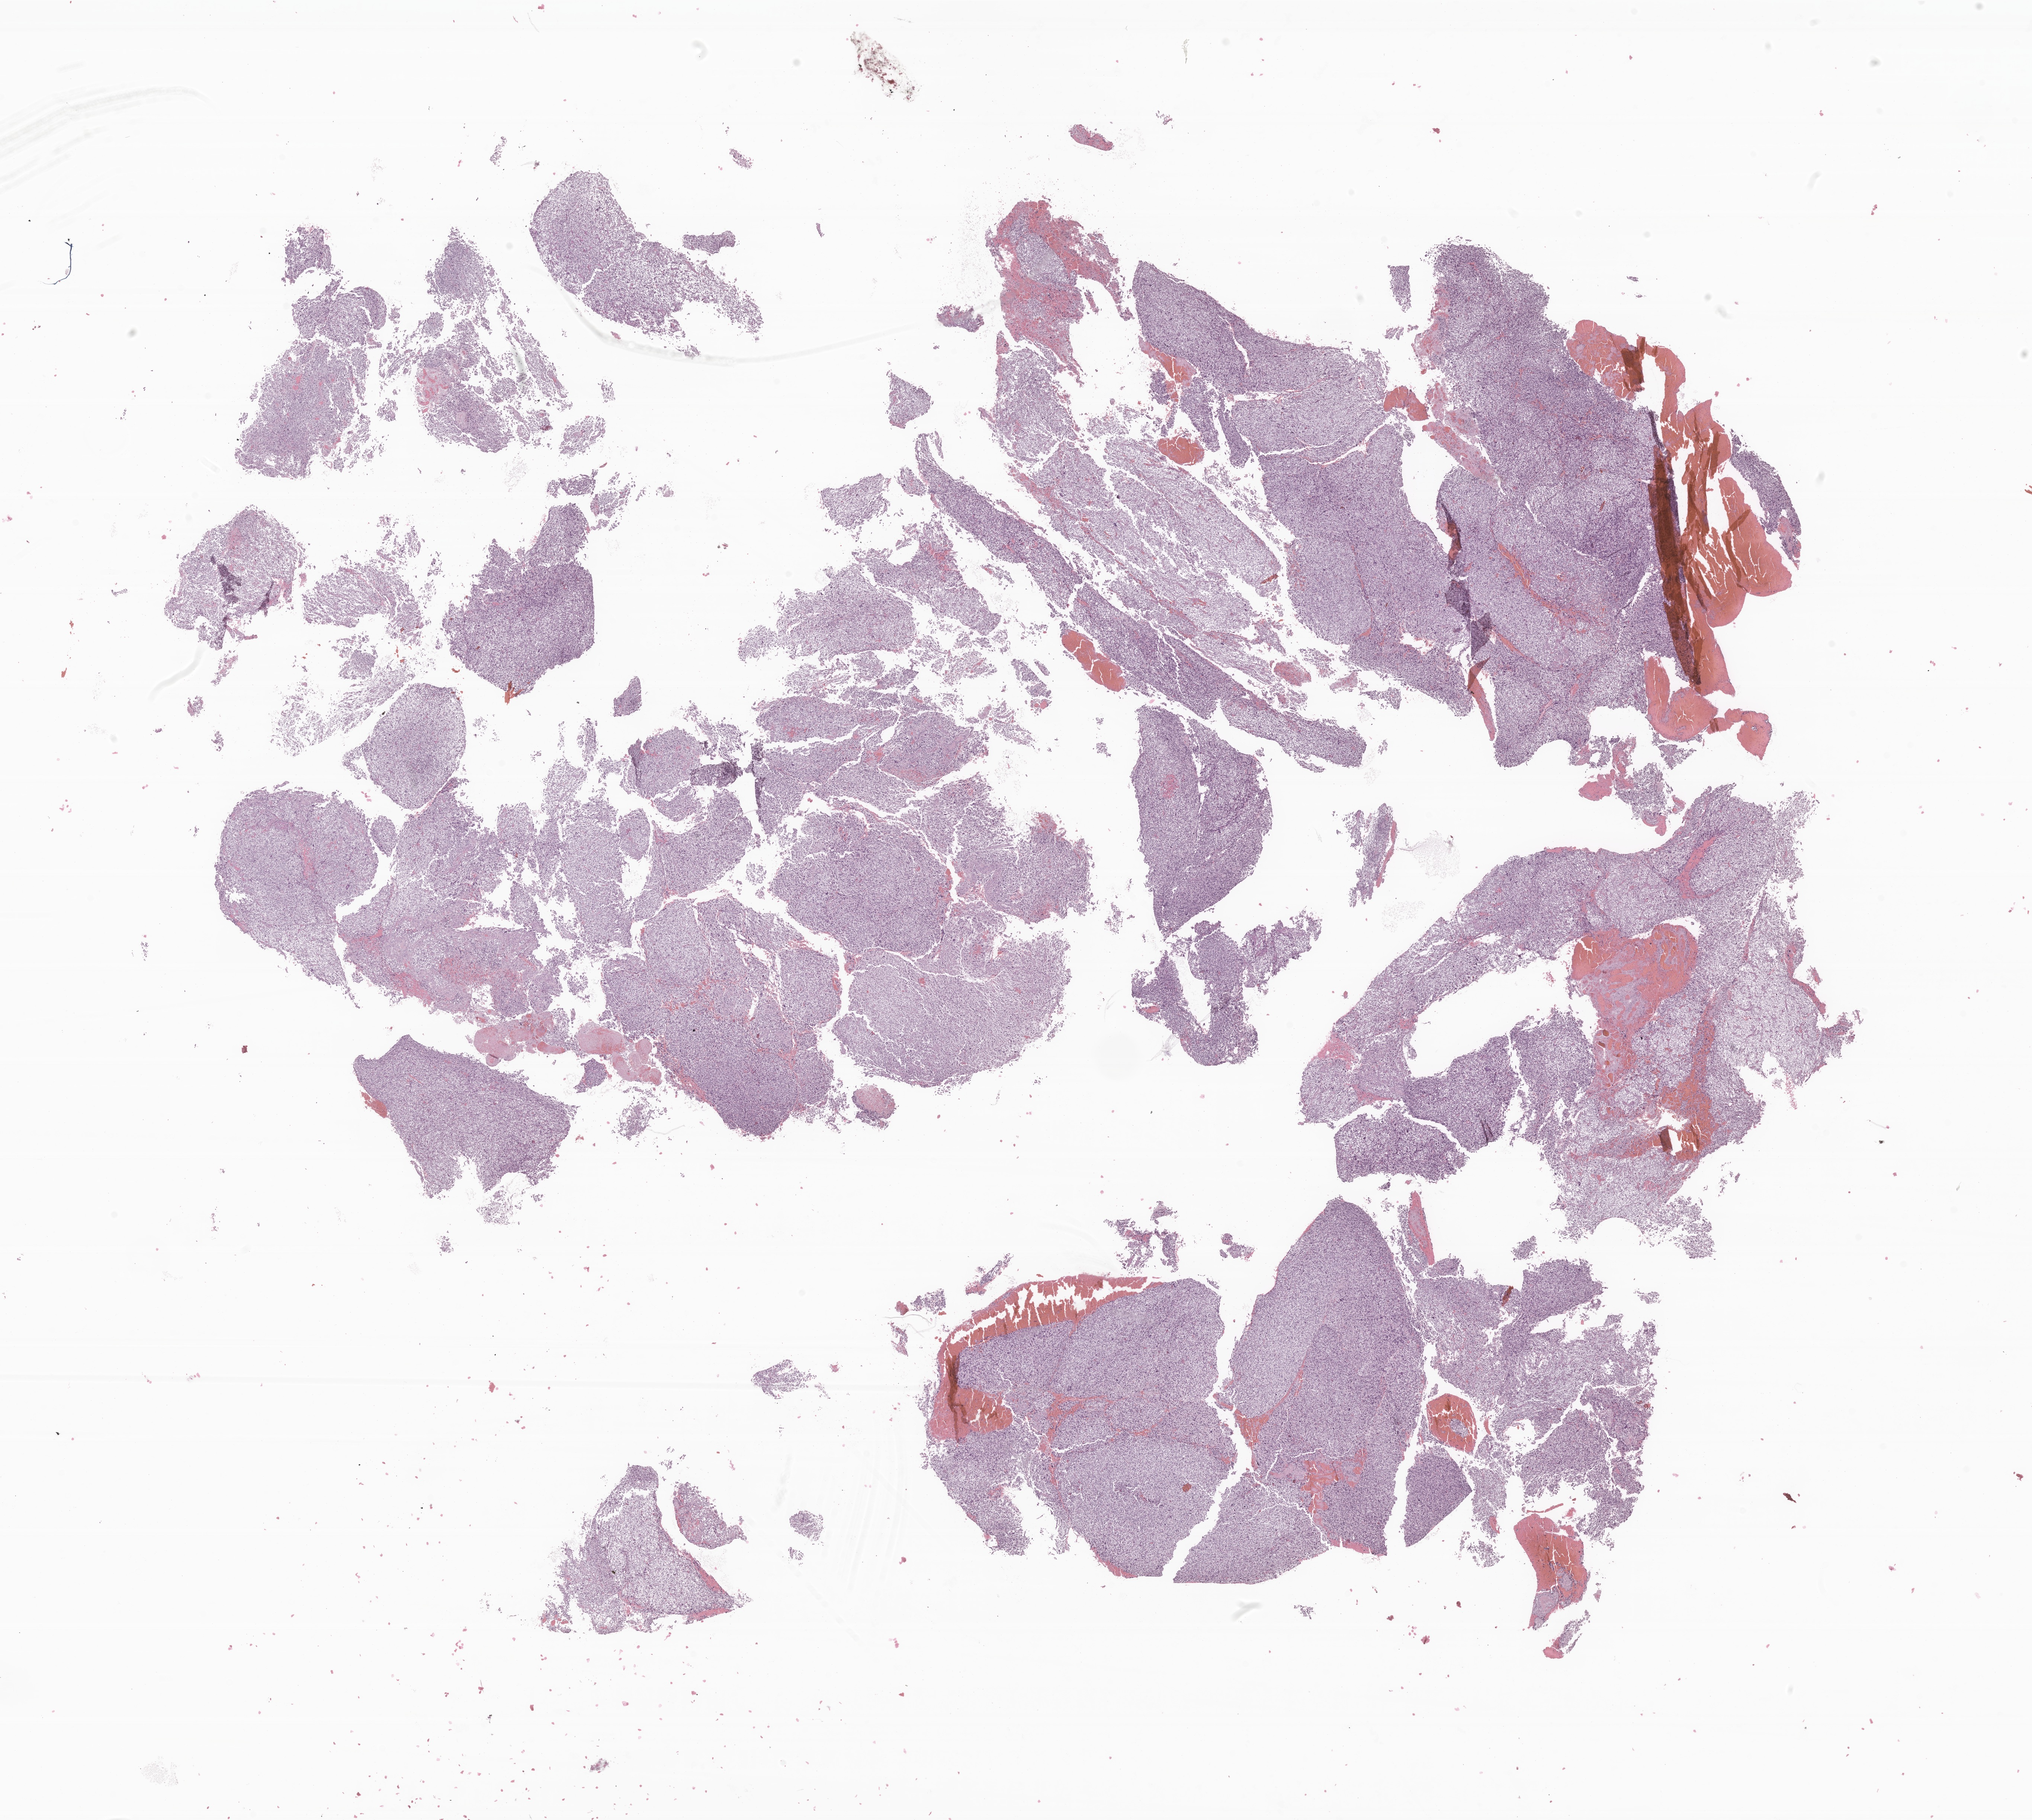
Digitized hematoxylin and eosin (H&E)-stained section of tumor tissue from the brain, a low-resolution overview of the entire scanned area, about 23.0 x 20.6 mm; formalin-fixed paraffin-embedded section. Patient male; age 138 months (11 years 6 months).
- recorded diagnosis: Neoplasm, malignant